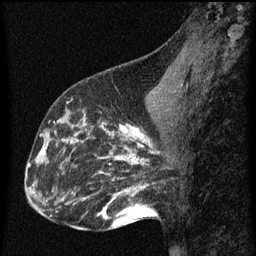
Breast MRI (dynamic contrast-enhanced), one sagittal slice; slice 27 of 60 in the series (ordered by position); dynamic contrast-enhanced series, image 2 of 3 at this slice position (ordered by acquisition); 1.5 T; TE 4.2 ms, TR 8 ms; 2 mm slice thickness; 256 × 256 image matrix, field of view 180 × 180 mm. Female patient, age 43 years.
Annotated regions visible in this slice (semi-automatic segmentation, software-assisted and operator-edited):
- analysis volume of interest (the breast-tissue region the enhancement analysis was run in; not a lesion): box from (x=53, y=104) to (x=100, y=155) px
- tumour enhancement mask (voxels above the 70 % enhancement threshold inside the analysis volume of interest): (x=59, y=114)–(x=88, y=143)